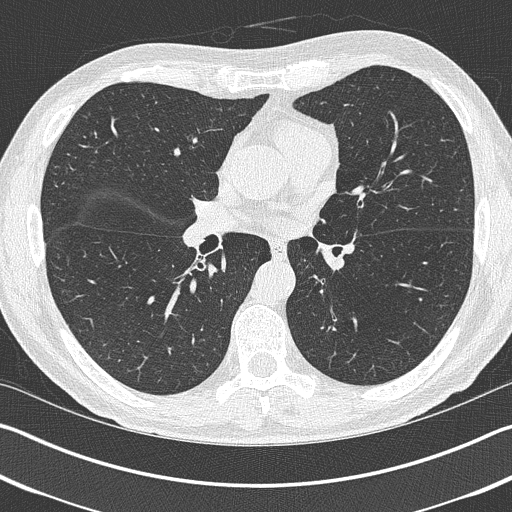
Low-dose screening chest CT, axial slice, baseline screening round, lung window (W 1500 / L -600 HU), 1 mm slice thickness, lung (sharp) reconstruction kernel (B50f), slice 181 of 402 in the series, 512 × 512 image matrix. Male, age 69 years at enrolment. Current smoker at enrolment.
• Expert-annotated lung lesion, bounding box <291,303,349,364> (left, top, right, bottom; pixels).
• Screening reader's record for this exam (one nodule recorded; not confirmed to be the boxed lesion): non-calcified nodule or mass ≥4 mm, left upper lobe, 19 × 19 mm, spiculated (stellate) margins, pre-existing on the prior screen: yes.
• Official screen result: positive, change unspecified: nodule(s) >= 4 mm or enlarging nodule(s), mass(es), or other non-specific abnormalities suspicious for lung cancer.